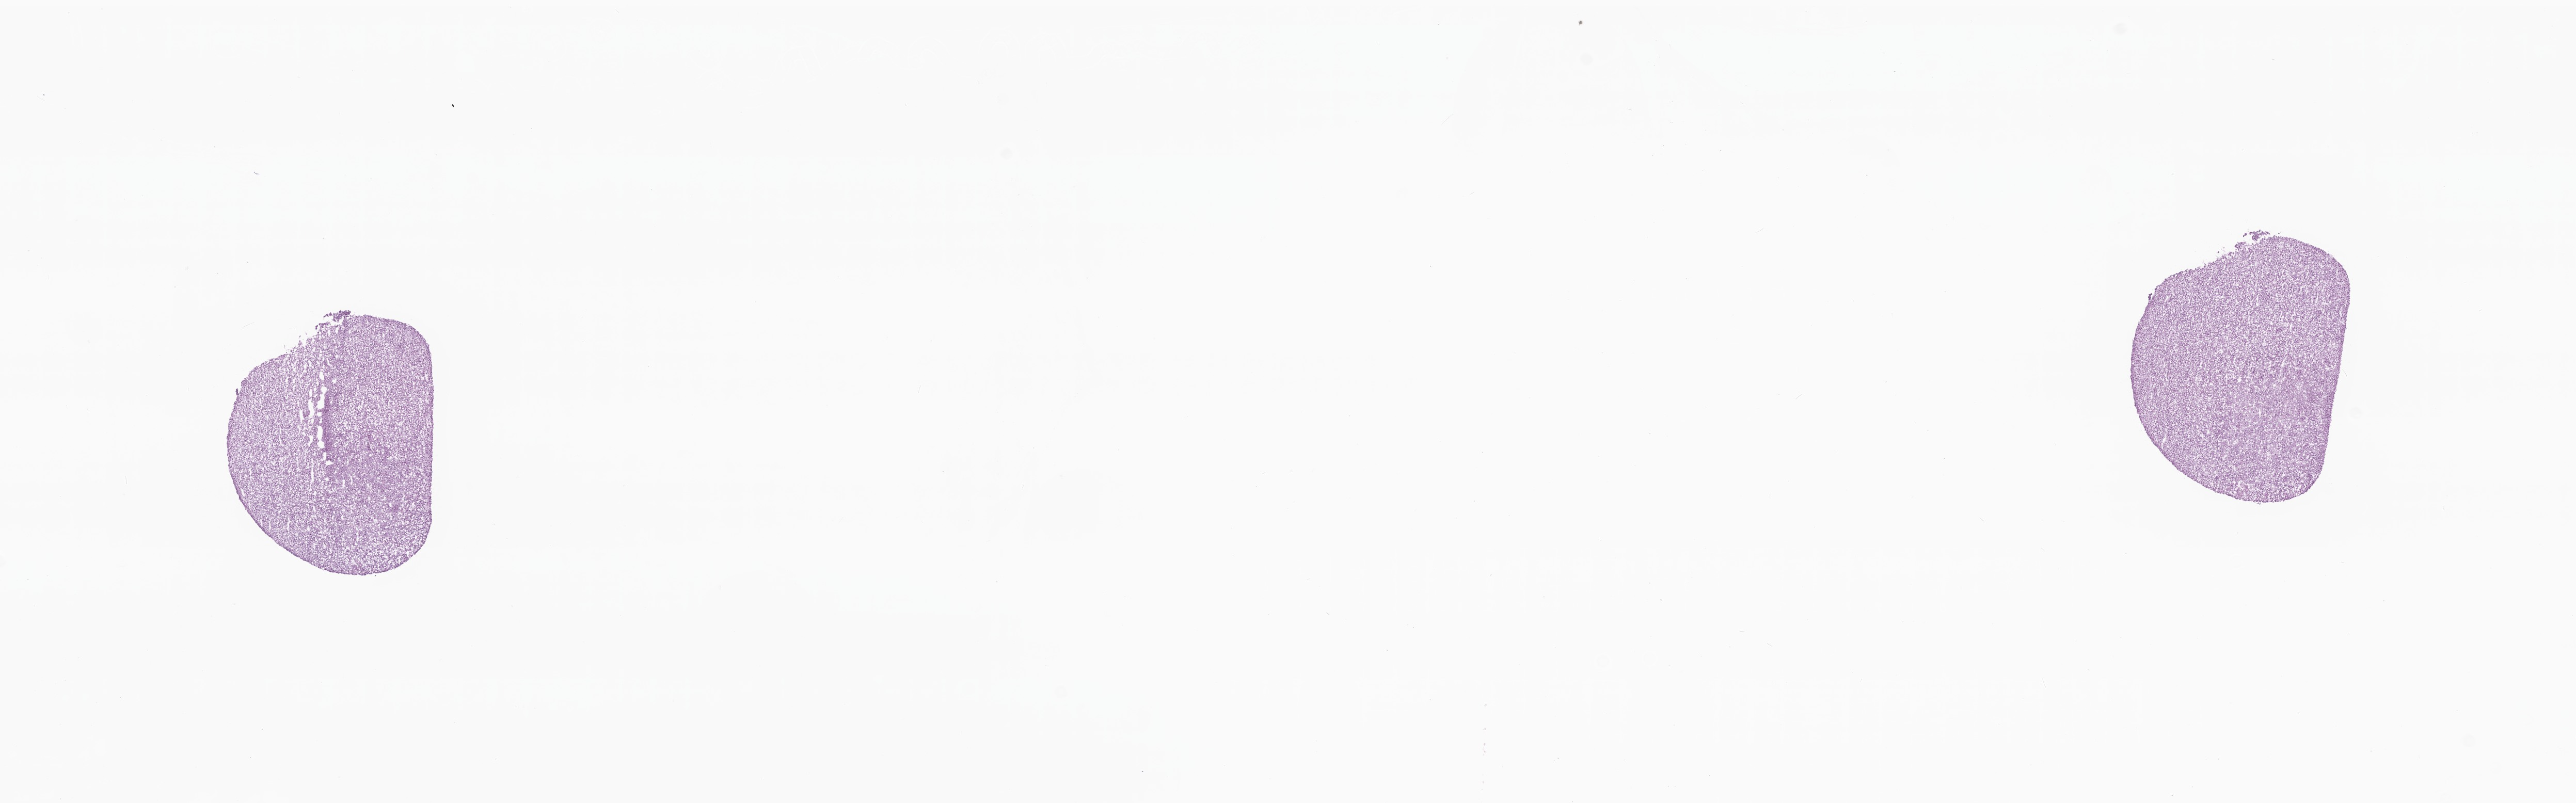
H&E whole-slide image — shown as a low-resolution overview of the whole scanned area (about 21.0 x 6.6 mm); frozen section; metastatic tumor tissue. Patient: female, age at initial diagnosis 36 years. Pathologist review of this section (percent, as recorded): tumor cells 90%, tumor nuclei 90%, stromal cells 10%, necrosis 0%, normal cells 0%. Infiltration values recorded for this section: lymphocyte infiltration 0%, monocyte infiltration 0%, neutrophil infiltration 0%.
* patient diagnosis (primary): Adenocarcinoma, NOS
* section: top of the tissue portion